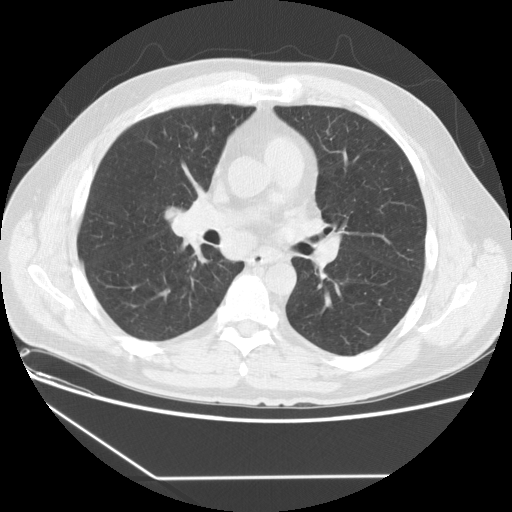
Low-dose screening chest CT, one axial slice; position 82 of 154 along the scan axis; reconstruction kernel STANDARD; 120 kVp; lung window (W 1500 / L -600 HU); 2.5 mm slice thickness; 512 × 512 image matrix, field of view 370 × 370 mm.
Structures marked on this image (outlined manually by an expert reader):
- lesion 1 (tumor, middle lobe of right lung): bounding box <166,208,206,244> (left, top, right, bottom; pixels)